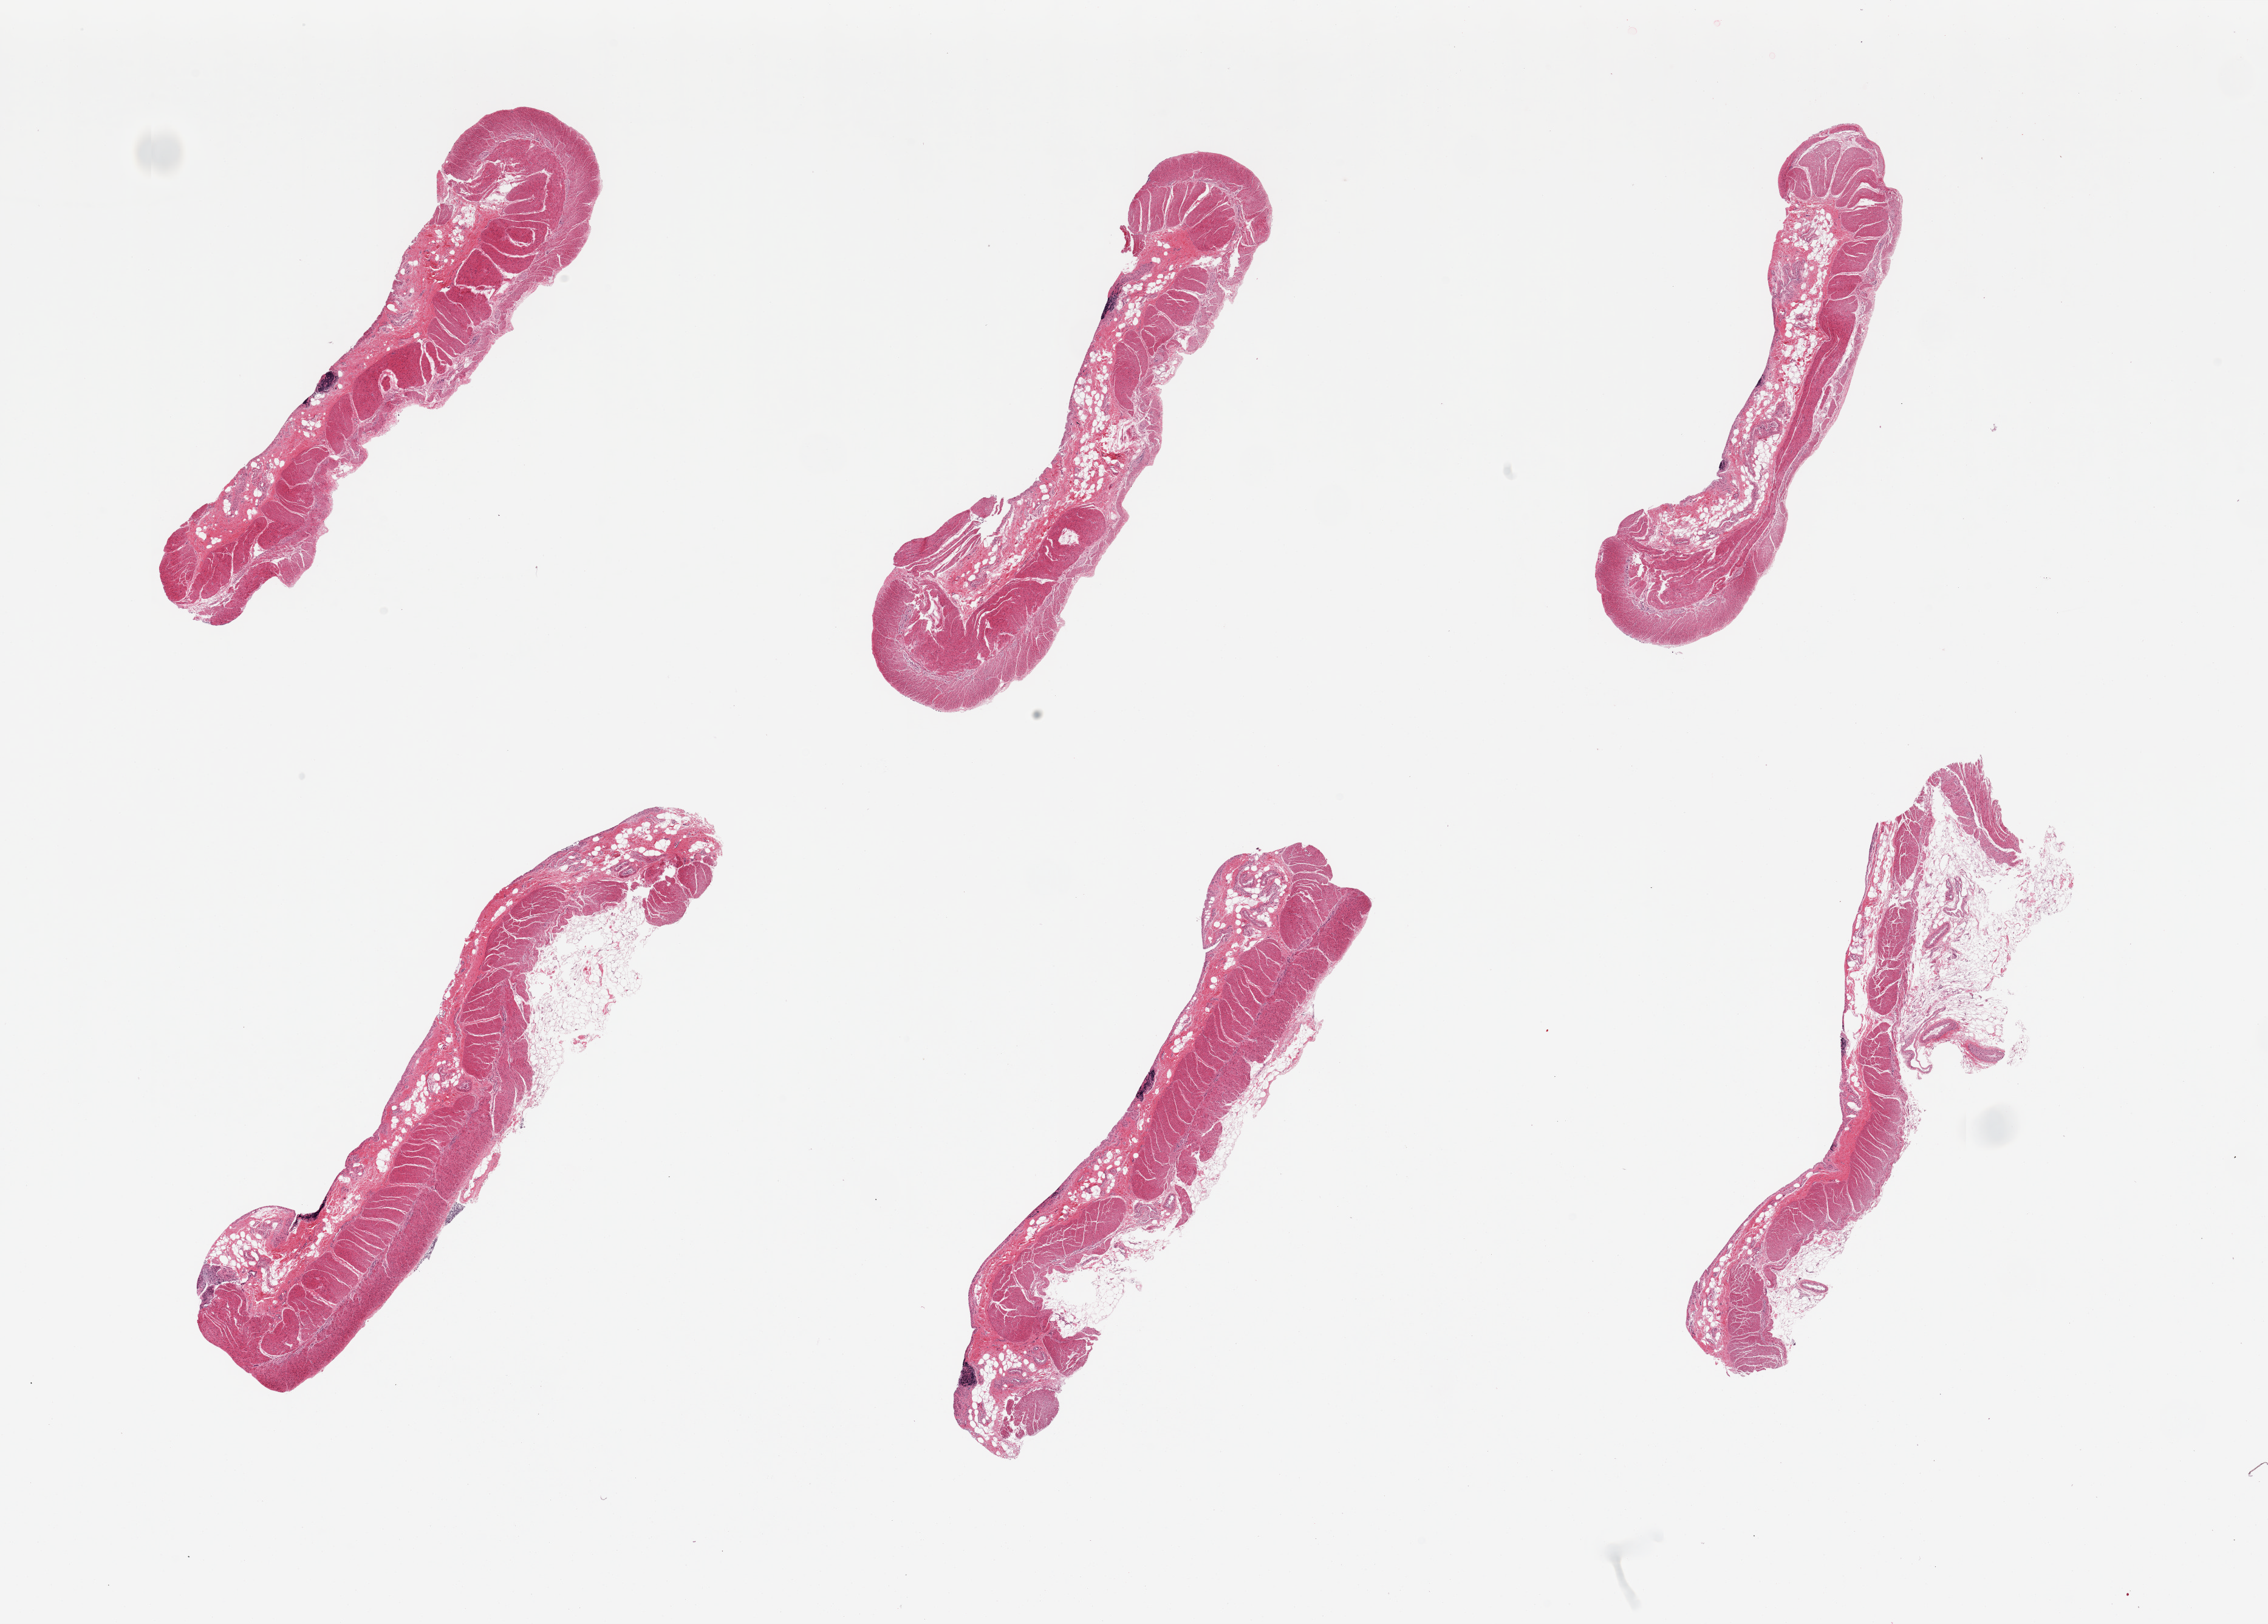
Haematoxylin and eosin whole-slide image — low-resolution overview of the scanned area, about 29.5 x 21.1 mm (slide scanned at 20x). PAXgene-fixed paraffin-embedded (PFPE) section. Target tissue: sigmoid colon. Donor tissue sample. Donor: female.
- pathologist's review note for this sample: 6 pieces, predominantly muscularis with few residual lymphoid aggregates